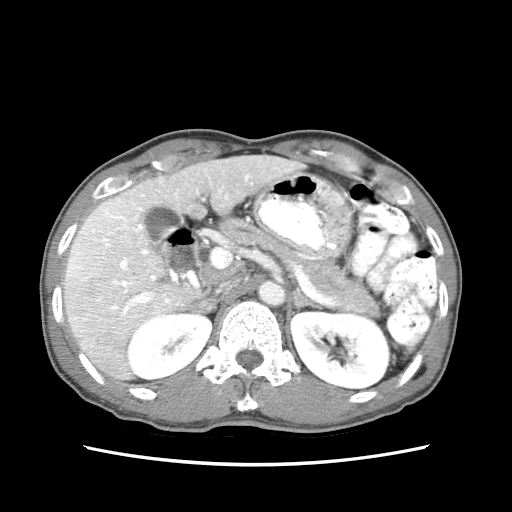
Contrast-enhanced abdominal CT (liver protocol), one axial slice; position 38 of 79 along the scan axis; reconstruction kernel STANDARD; soft-tissue window (W 400 / L 40 HU); 512 × 512 image matrix, field of view 320 × 320 mm. Case-level facts recorded for this patient, not image findings: diagnosis: hepatocellular carcinoma (patient treated with transarterial chemoembolisation; whether this scan precedes or follows treatment is not stated here); TNM stage (as recorded): Stage-IIIB.
Outlined on this slice (semi-automatically segmented with operator editing):
- liver parenchyma outside the tumour (the mass and vessels are separate outlines, so this box may not span the whole liver): bounding box (x1, y1, x2, y2) in pixels: (62, 152, 305, 384)
- mass: (67, 250, 102, 281)
- liver vessels: (67, 162, 264, 320)